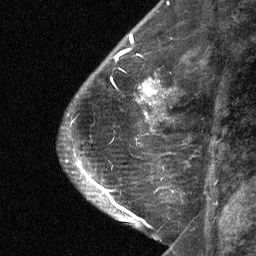
Breast MRI (dynamic contrast-enhanced), one sagittal slice. Slice 21 of 64 in the series (ordered by position). Dynamic contrast-enhanced study with each time point stored as its own series, time point 2 of 3 at this slice position (early post-contrast, ordered by acquisition time). 1.5 T. TE 4.8 ms, TR 27 ms. 2 mm slice thickness. 256 × 256 image matrix, field of view 180 × 180 mm. Female patient, age 59 years. From the clinical record (not read from this slice): setting: breast cancer imaged before/during neoadjuvant chemotherapy; receptor status: triple-negative.
Annotated regions visible in this slice (semi-automatic segmentation, software-assisted and operator-edited):
- analysis volume of interest (the breast-tissue region the enhancement analysis was run in; not a lesion): bounding box (x1, y1, x2, y2) in pixels: (122, 58, 176, 109)
- tumour enhancement mask (voxels above the 90 % enhancement threshold inside the analysis volume of interest): (139, 78, 159, 97)